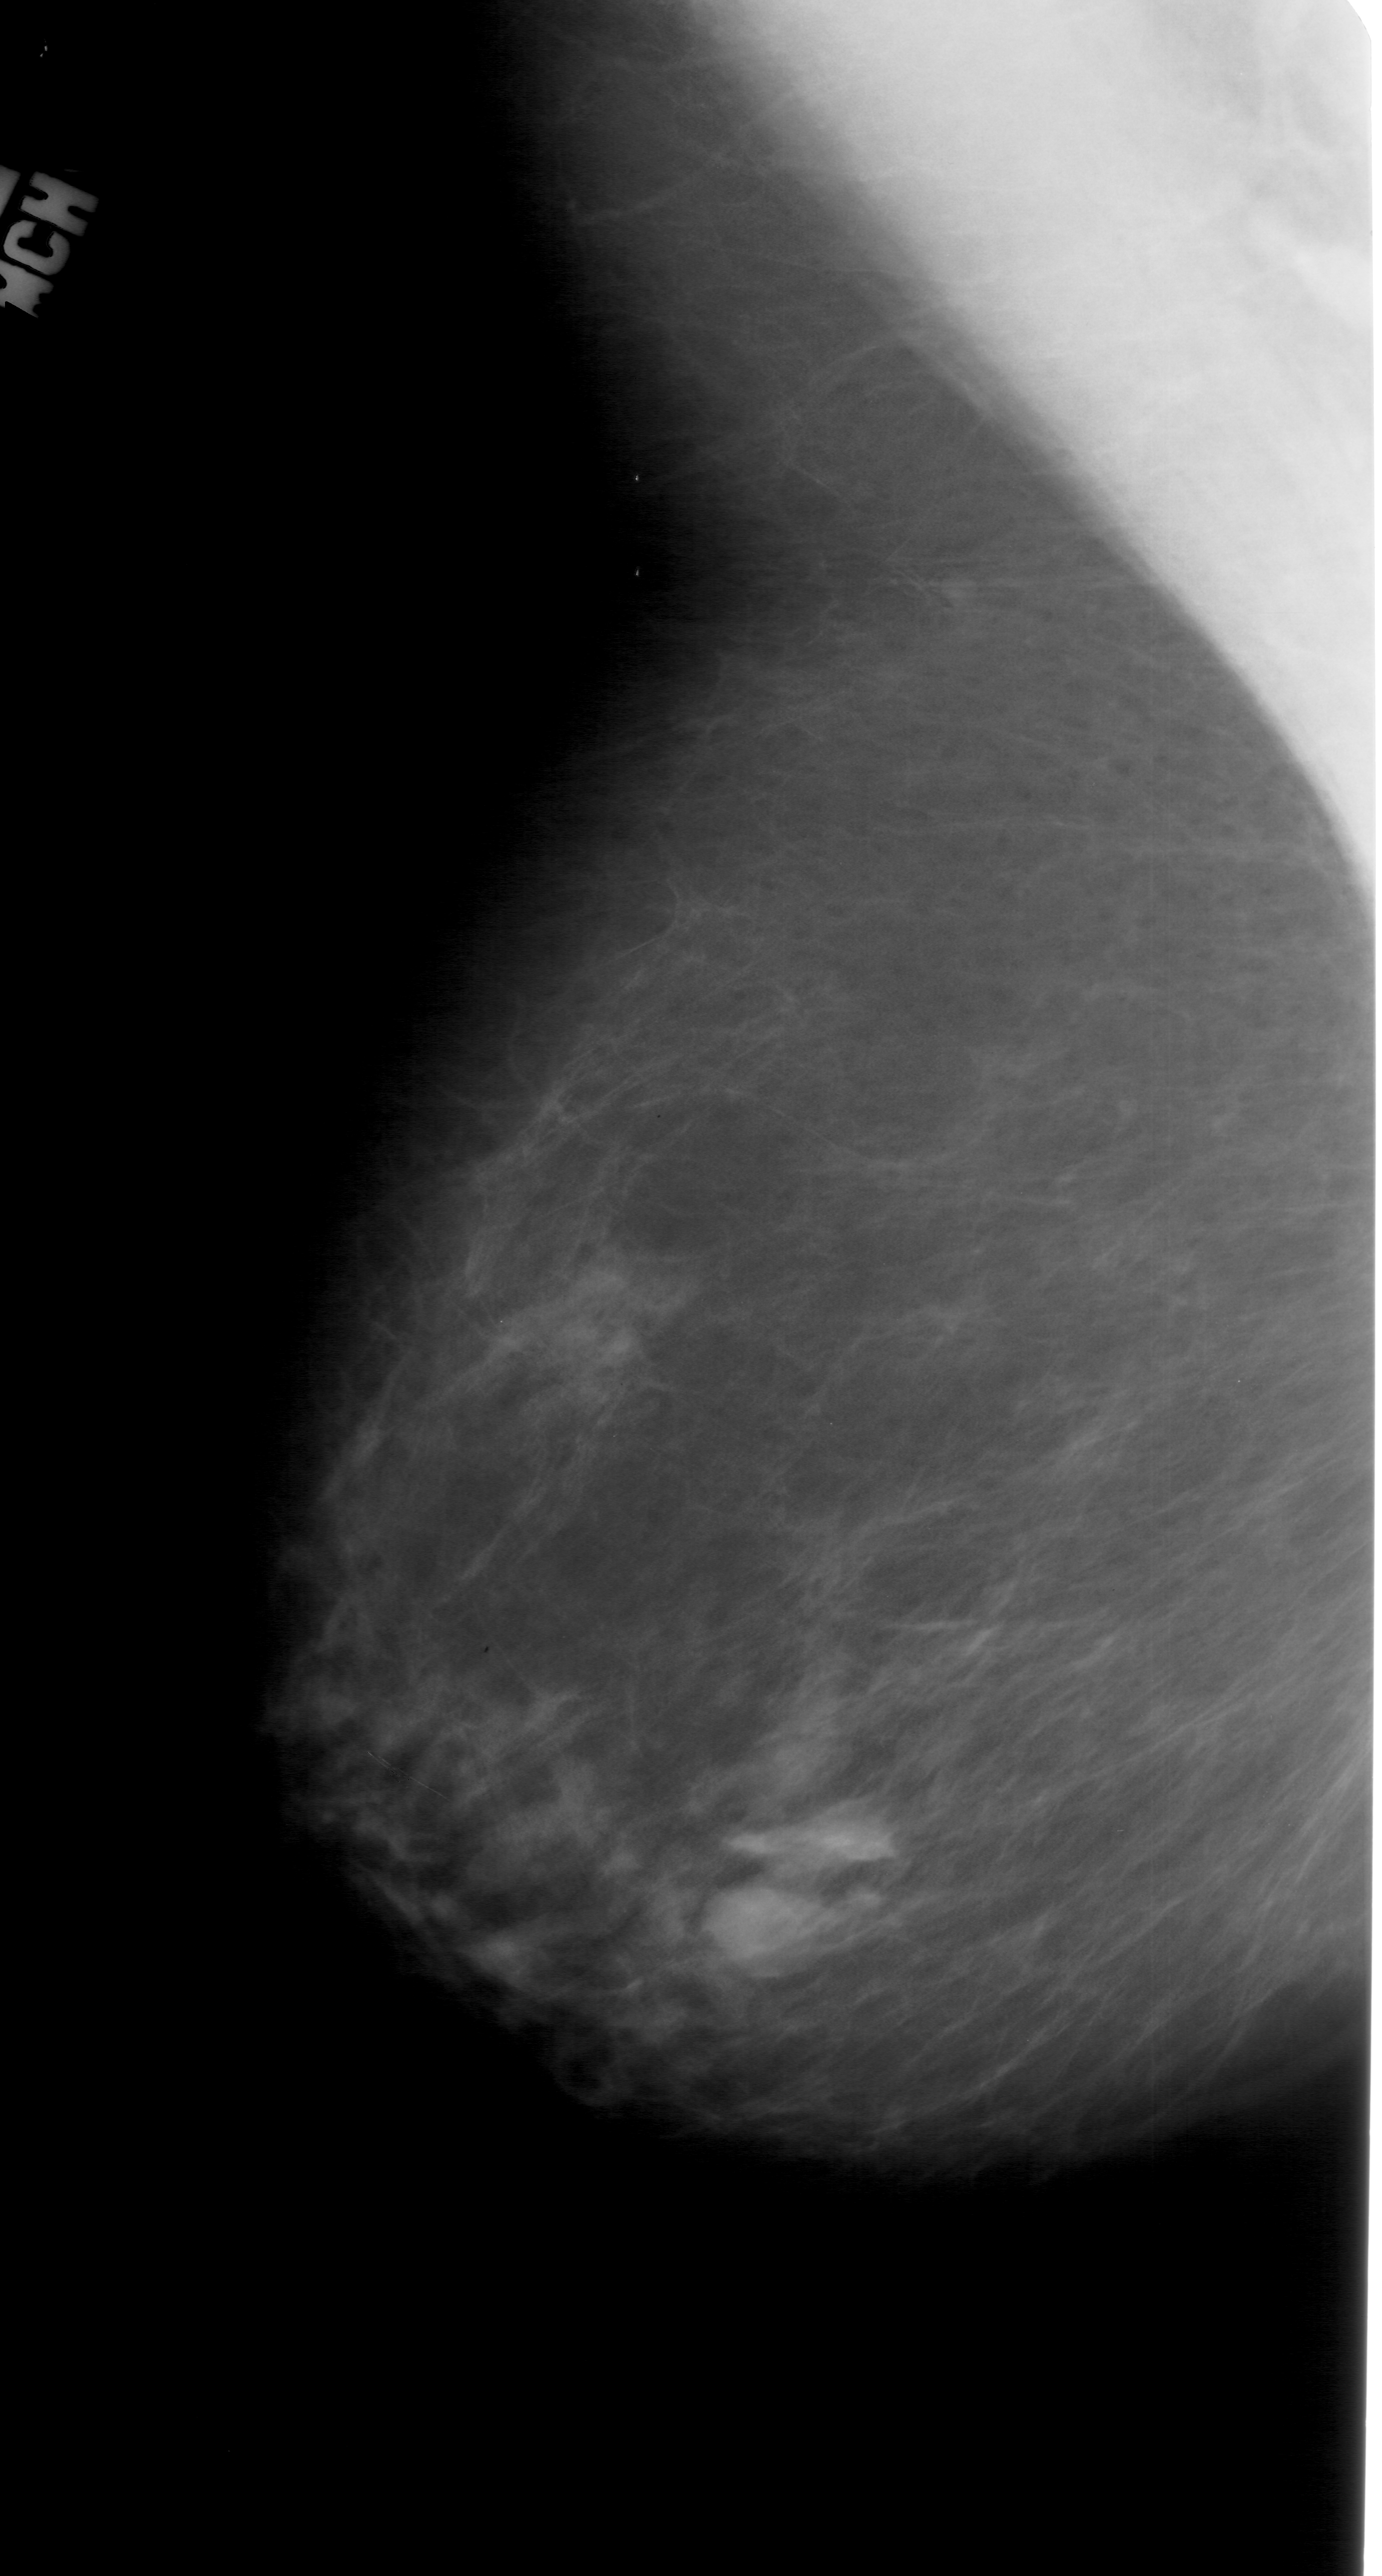
Digitized screen-film mammogram; left breast; MLO view; BI-RADS breast density category 2 (scale 1–4).
Radiologist-marked abnormalities on this image: mass, shape lobulated, margins ill defined; BI-RADS assessment category 4; subtlety rating 5 on a 1 (subtle) to 5 (obvious) scale; pathology (as recorded): benign.